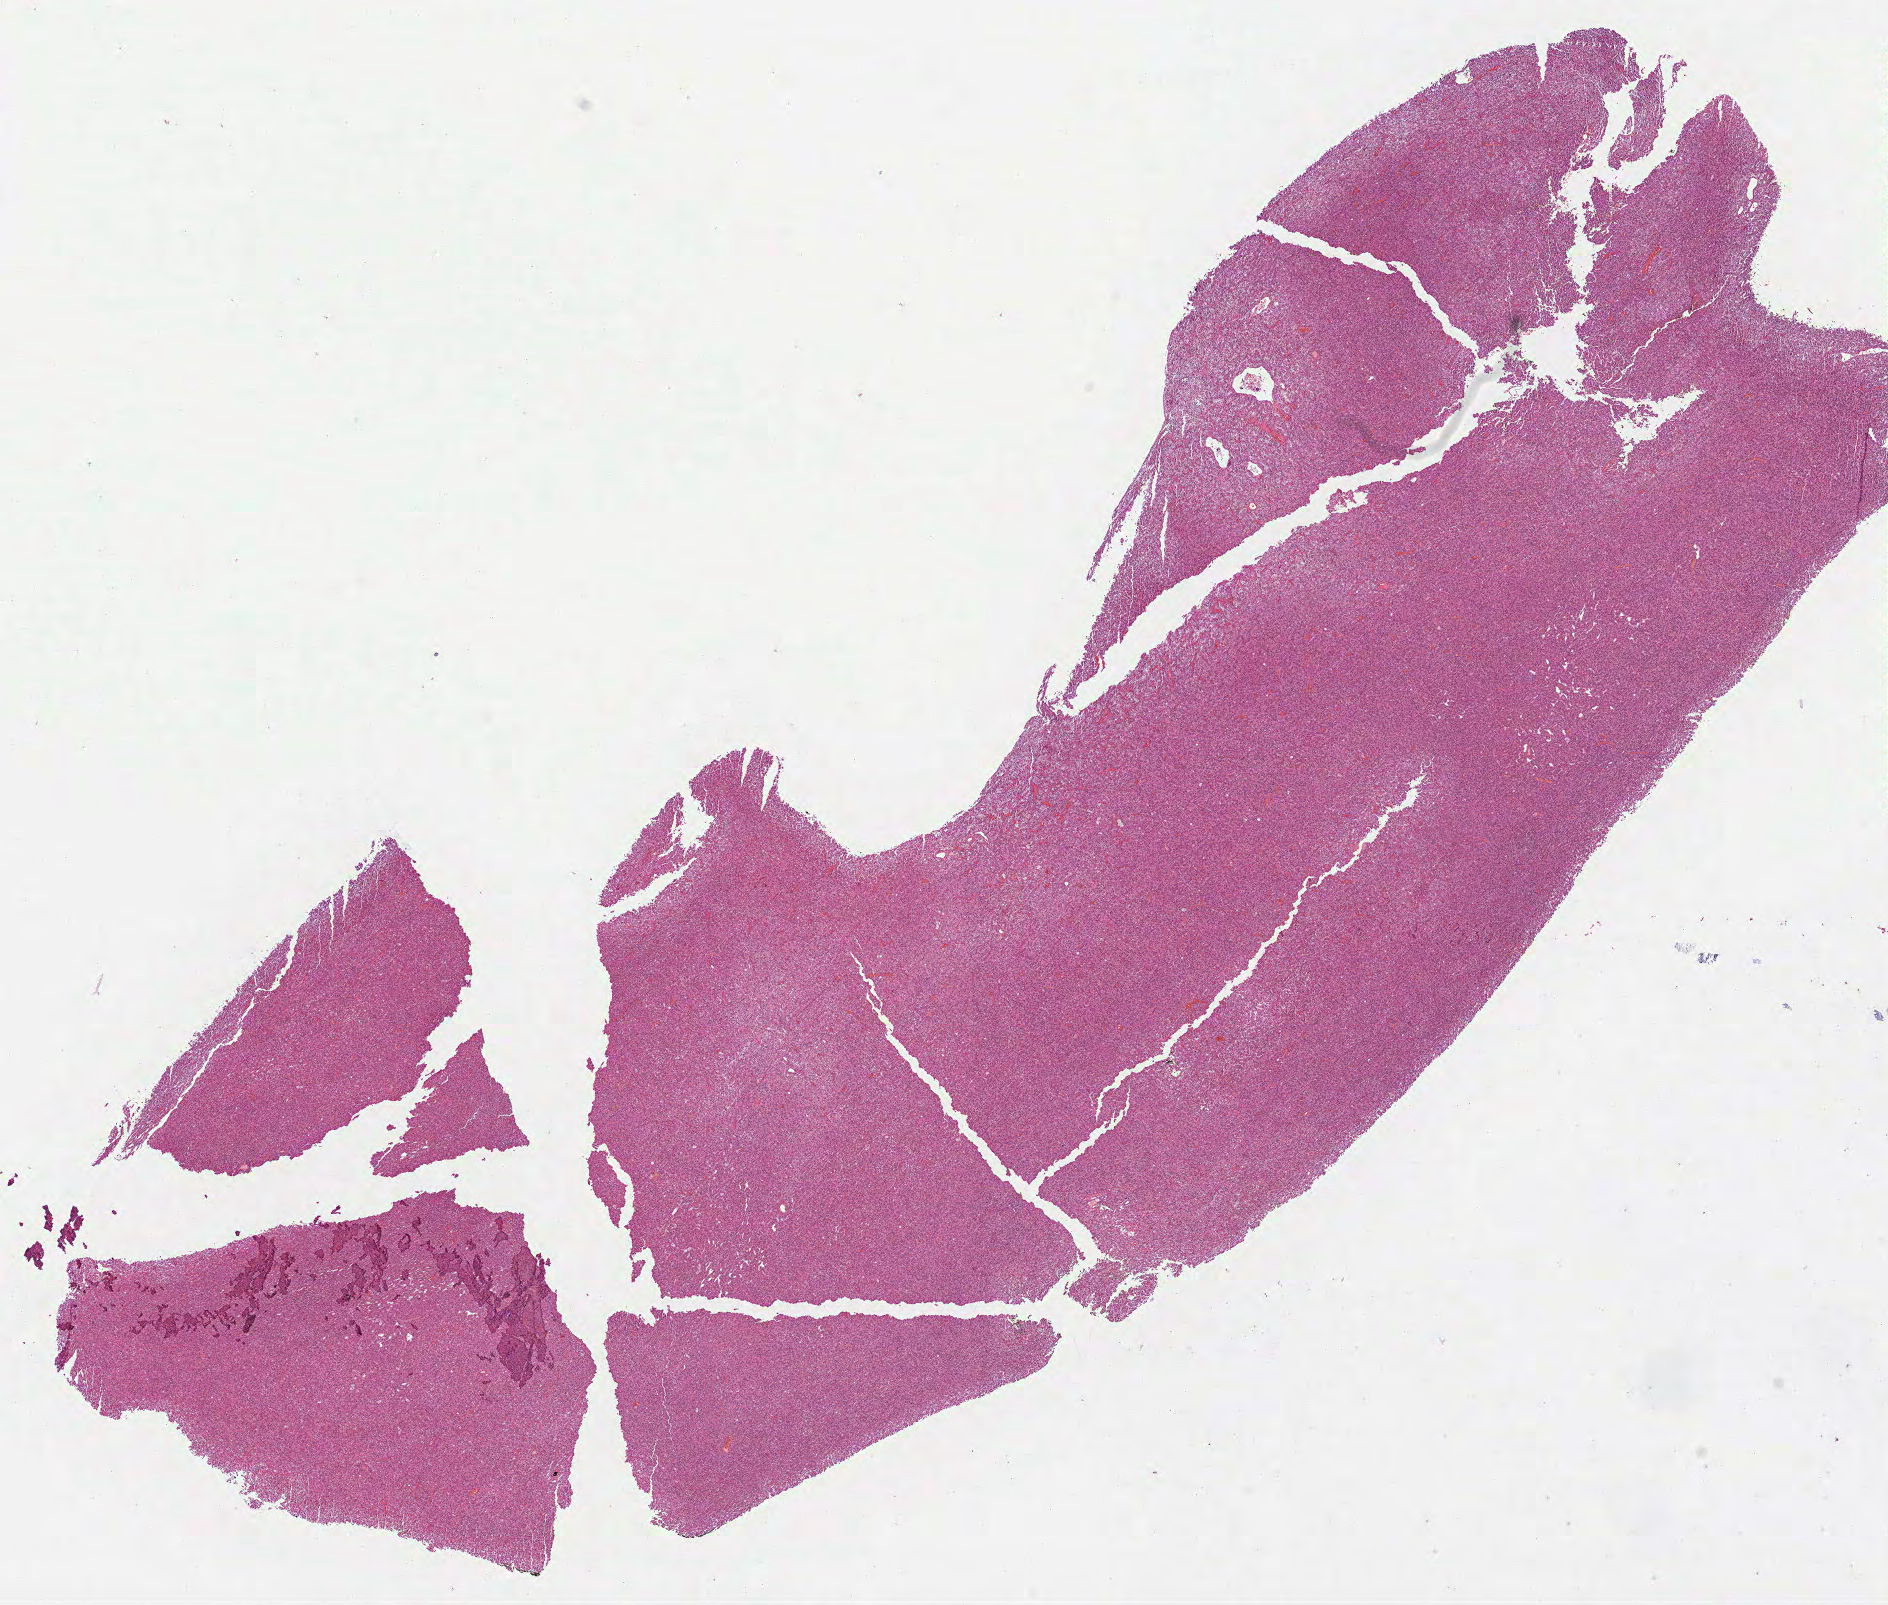
Hematoxylin and eosin (H&E) stained whole-slide image — a low-resolution overview of the entire scanned area, about 15.2 x 12.9 mm (from a 40x scan); formalin-fixed paraffin-embedded (FFPE) diagnostic section; primary tumour sample from the kidney. Male patient; age at initial diagnosis 47 years.
AJCC pathologic stage: I (7th edition). Laterality: right. Histologic diagnosis: Papillary adenocarcinoma, NOS. TNM: T1a NX MX.